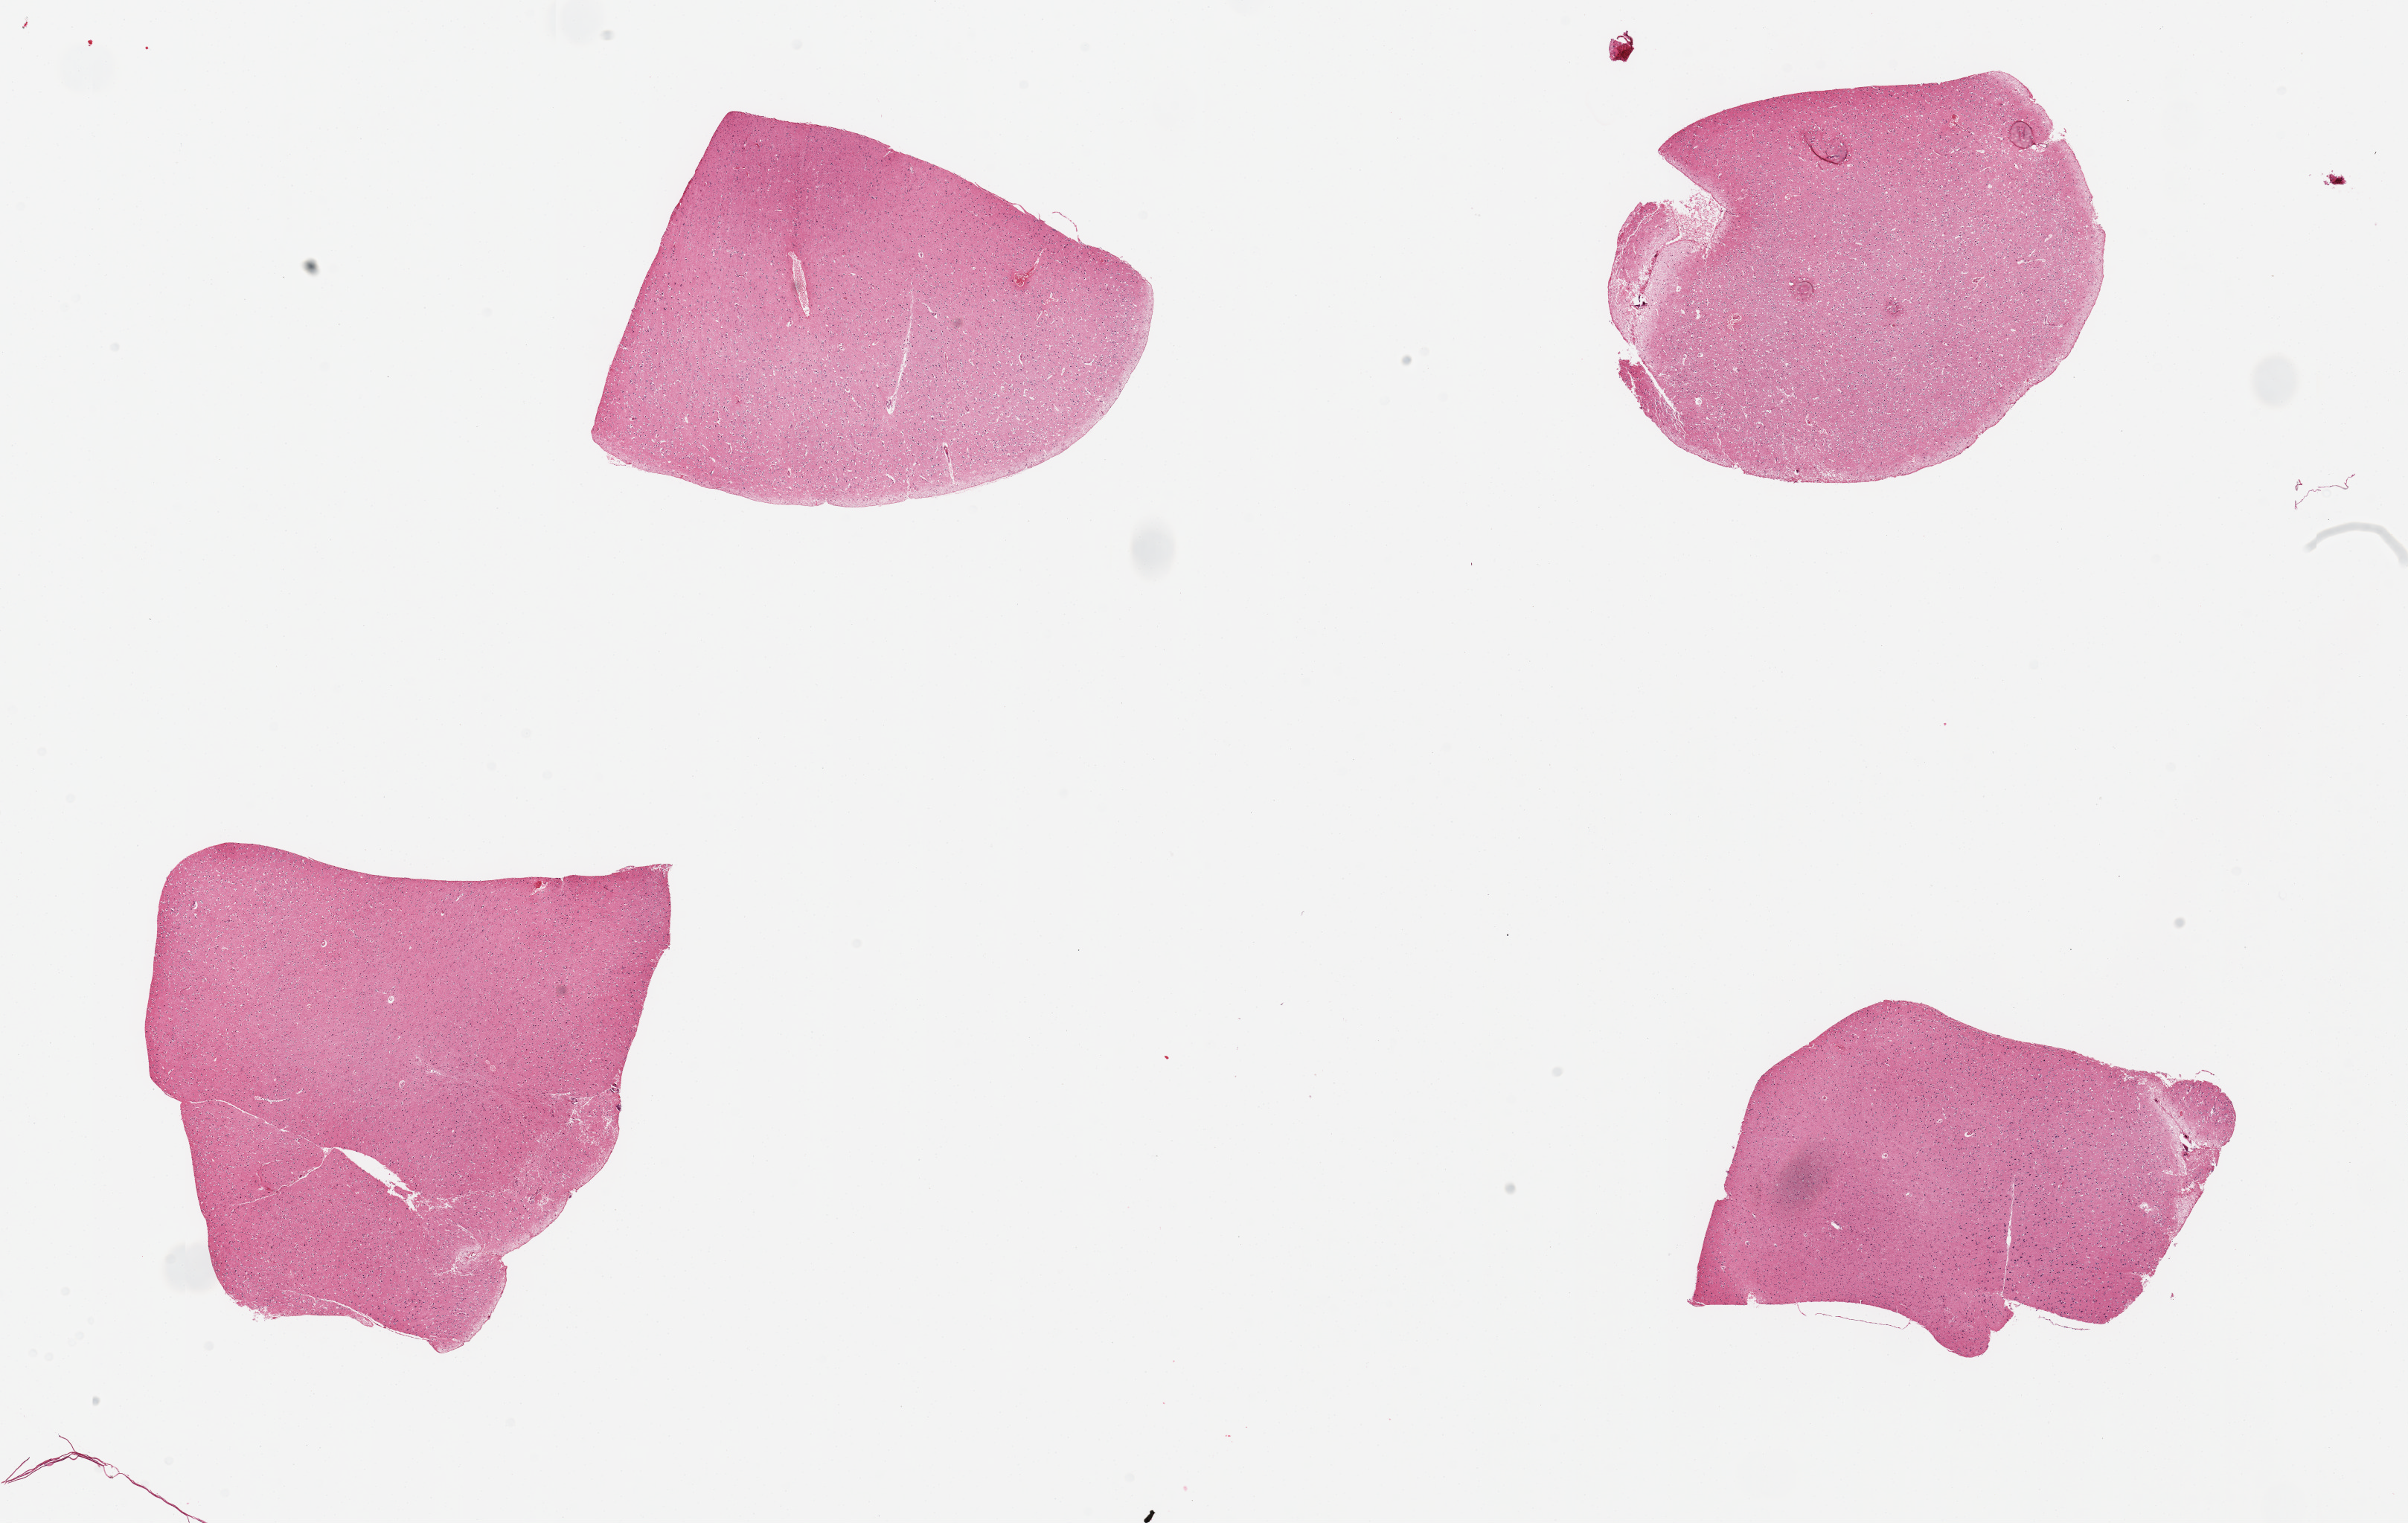
Whole-slide image, haematoxylin and eosin stain, brightfield, a low-resolution overview of the entire scanned area, about 25.6 x 16.2 mm. PAXgene-fixed paraffin-embedded (PFPE) section. Sampled site (target tissue): cerebral cortex. Tissue donor sample. Donor: male.
Review note (as recorded): 4 pieces.